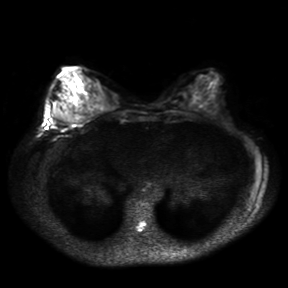
Breast MRI, one axial slice; slice 12 of 30 in the series (ordered by position); diffusion-weighted series; image 2 of 4 stored at this slice position (different b-values; order by instance number); 3 T; 4 mm slice thickness; 288 × 288 image matrix, field of view 360 × 360 mm. Female patient.
Outlined on this slice (expert manual segmentation):
- tumour on diffusion-weighted imaging: bounding box <54,107,63,121> (left, top, right, bottom; pixels)